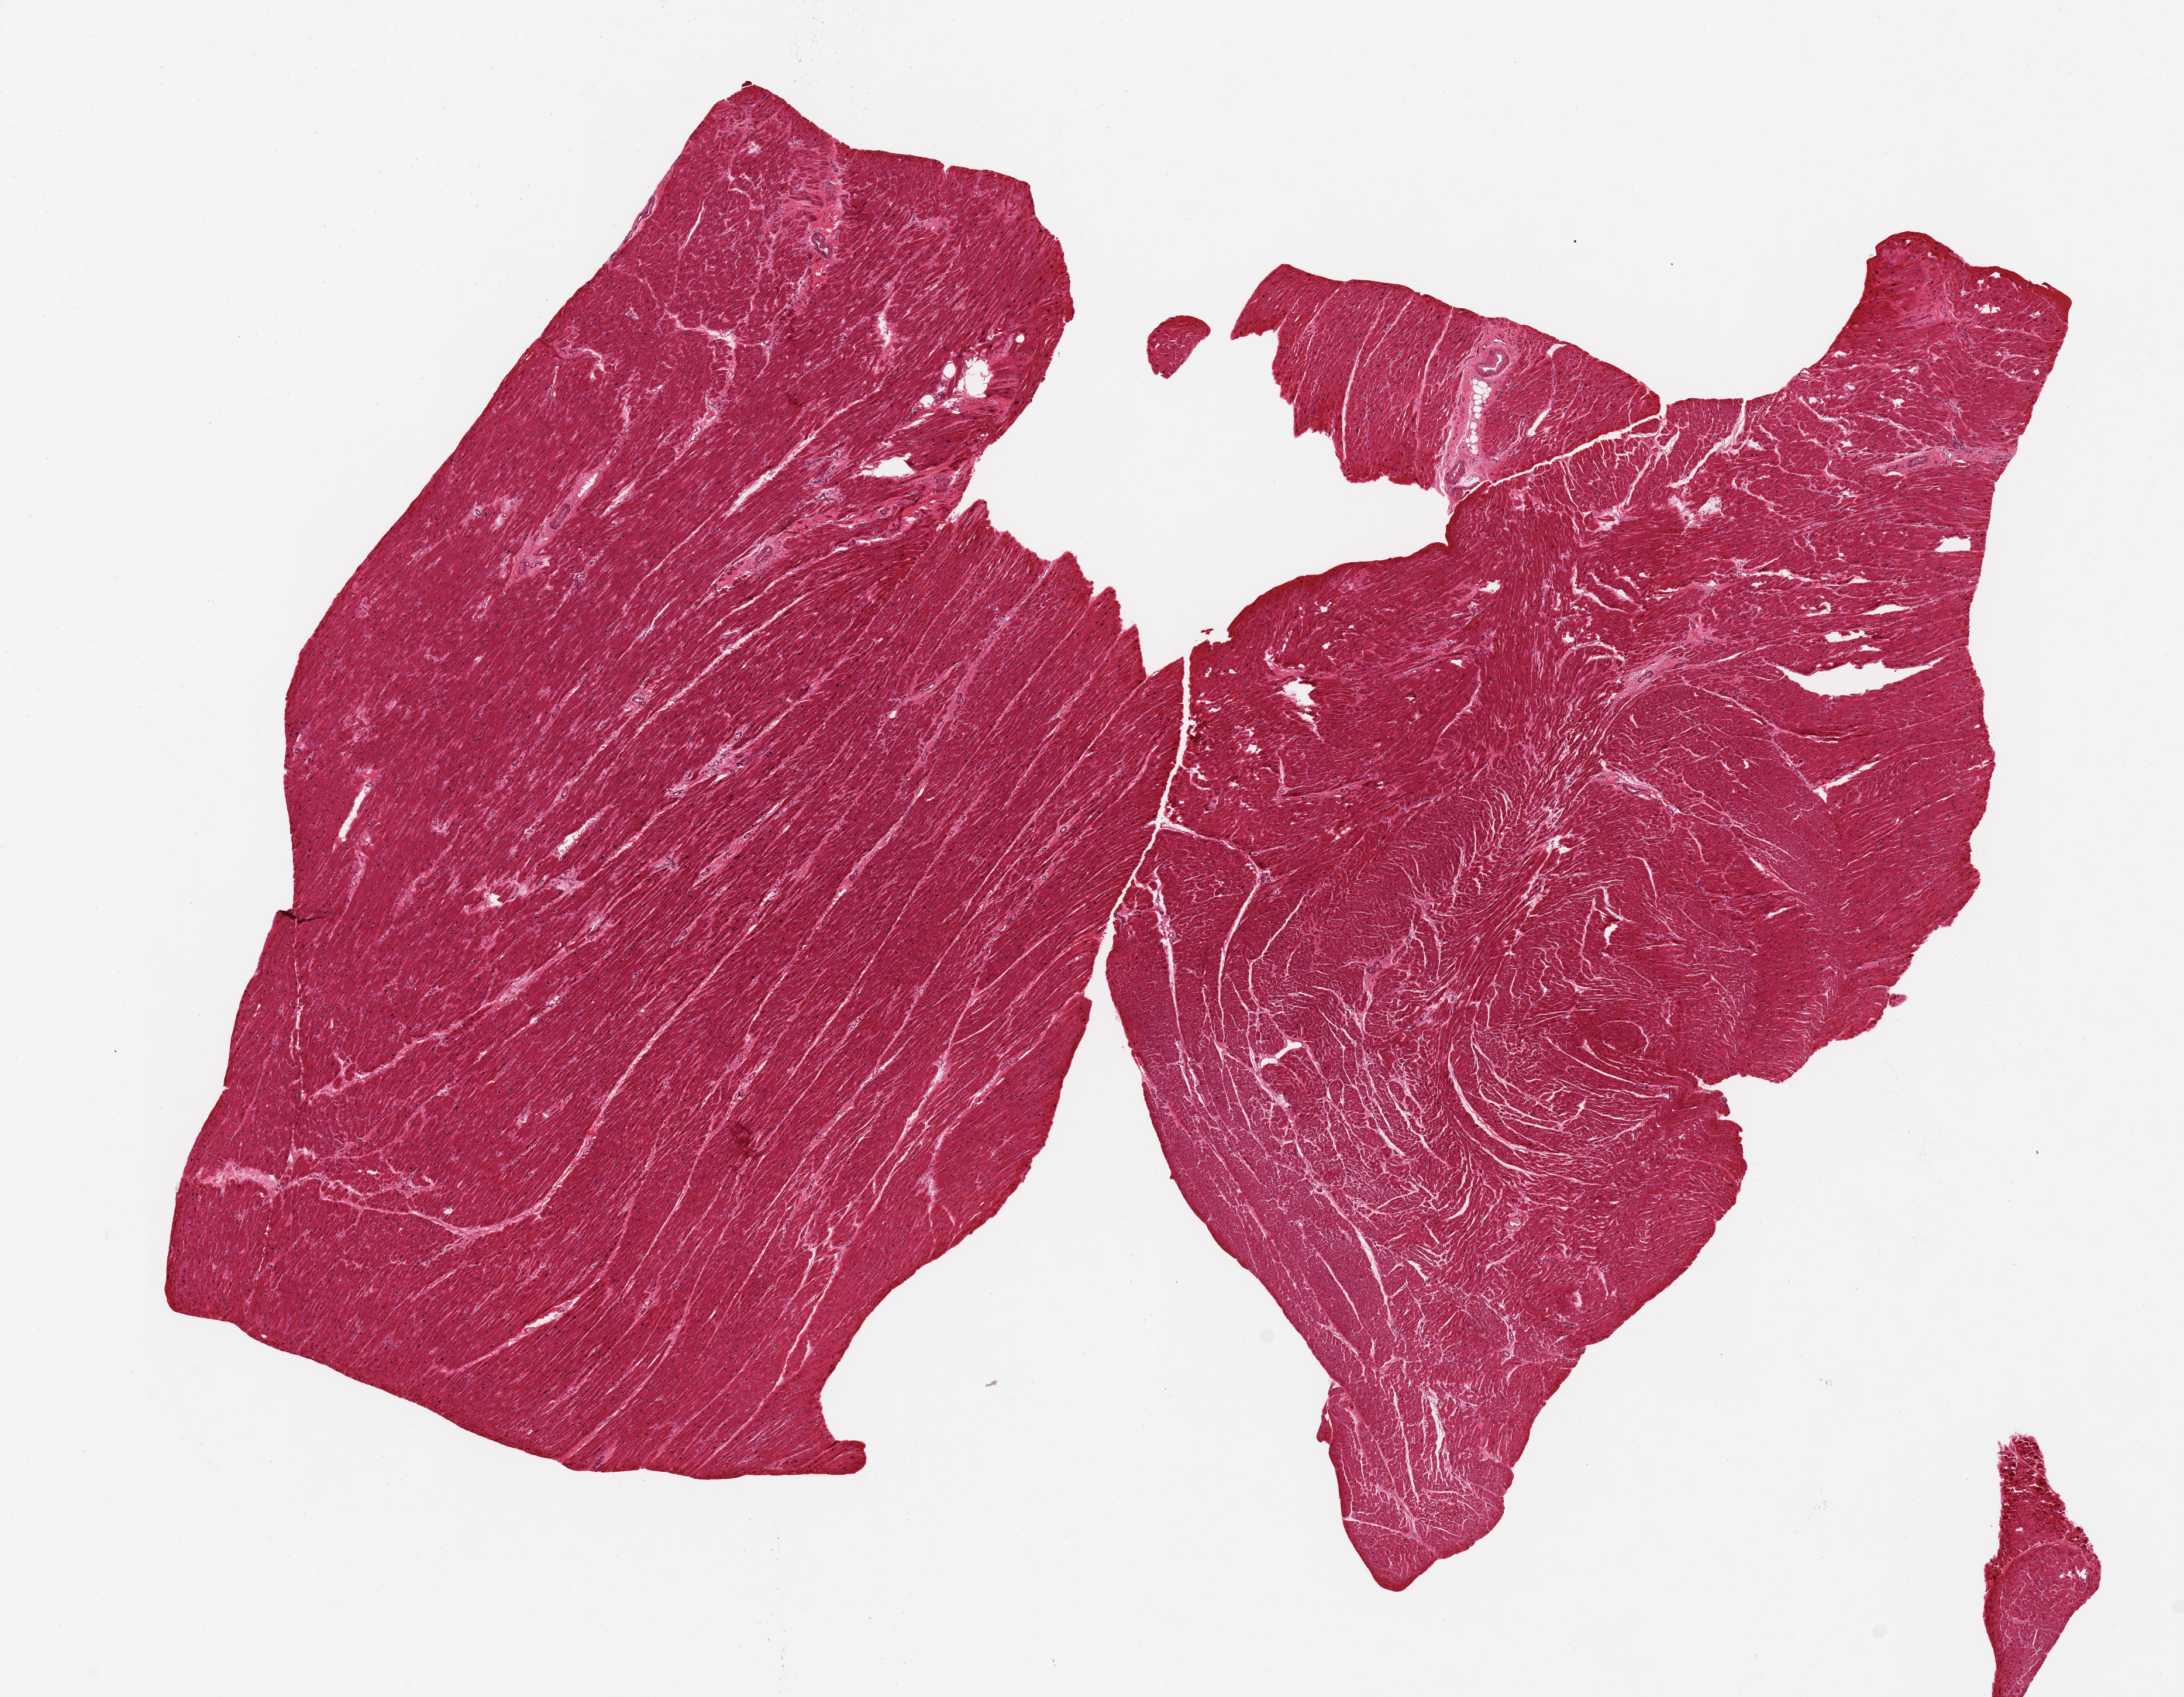
H&E whole-slide image, whole scanned area (about 14.8 x 11.5 mm, acquisition: 20x scan) shown as a low-resolution overview, PAXgene-fixed paraffin-embedded (PFPE) section, target tissue: heart, donor tissue sample. Male donor.
Review note (as recorded): 2 aliquots, ~10x5mm. Mild ischemic changes, focal contraction banding noted.